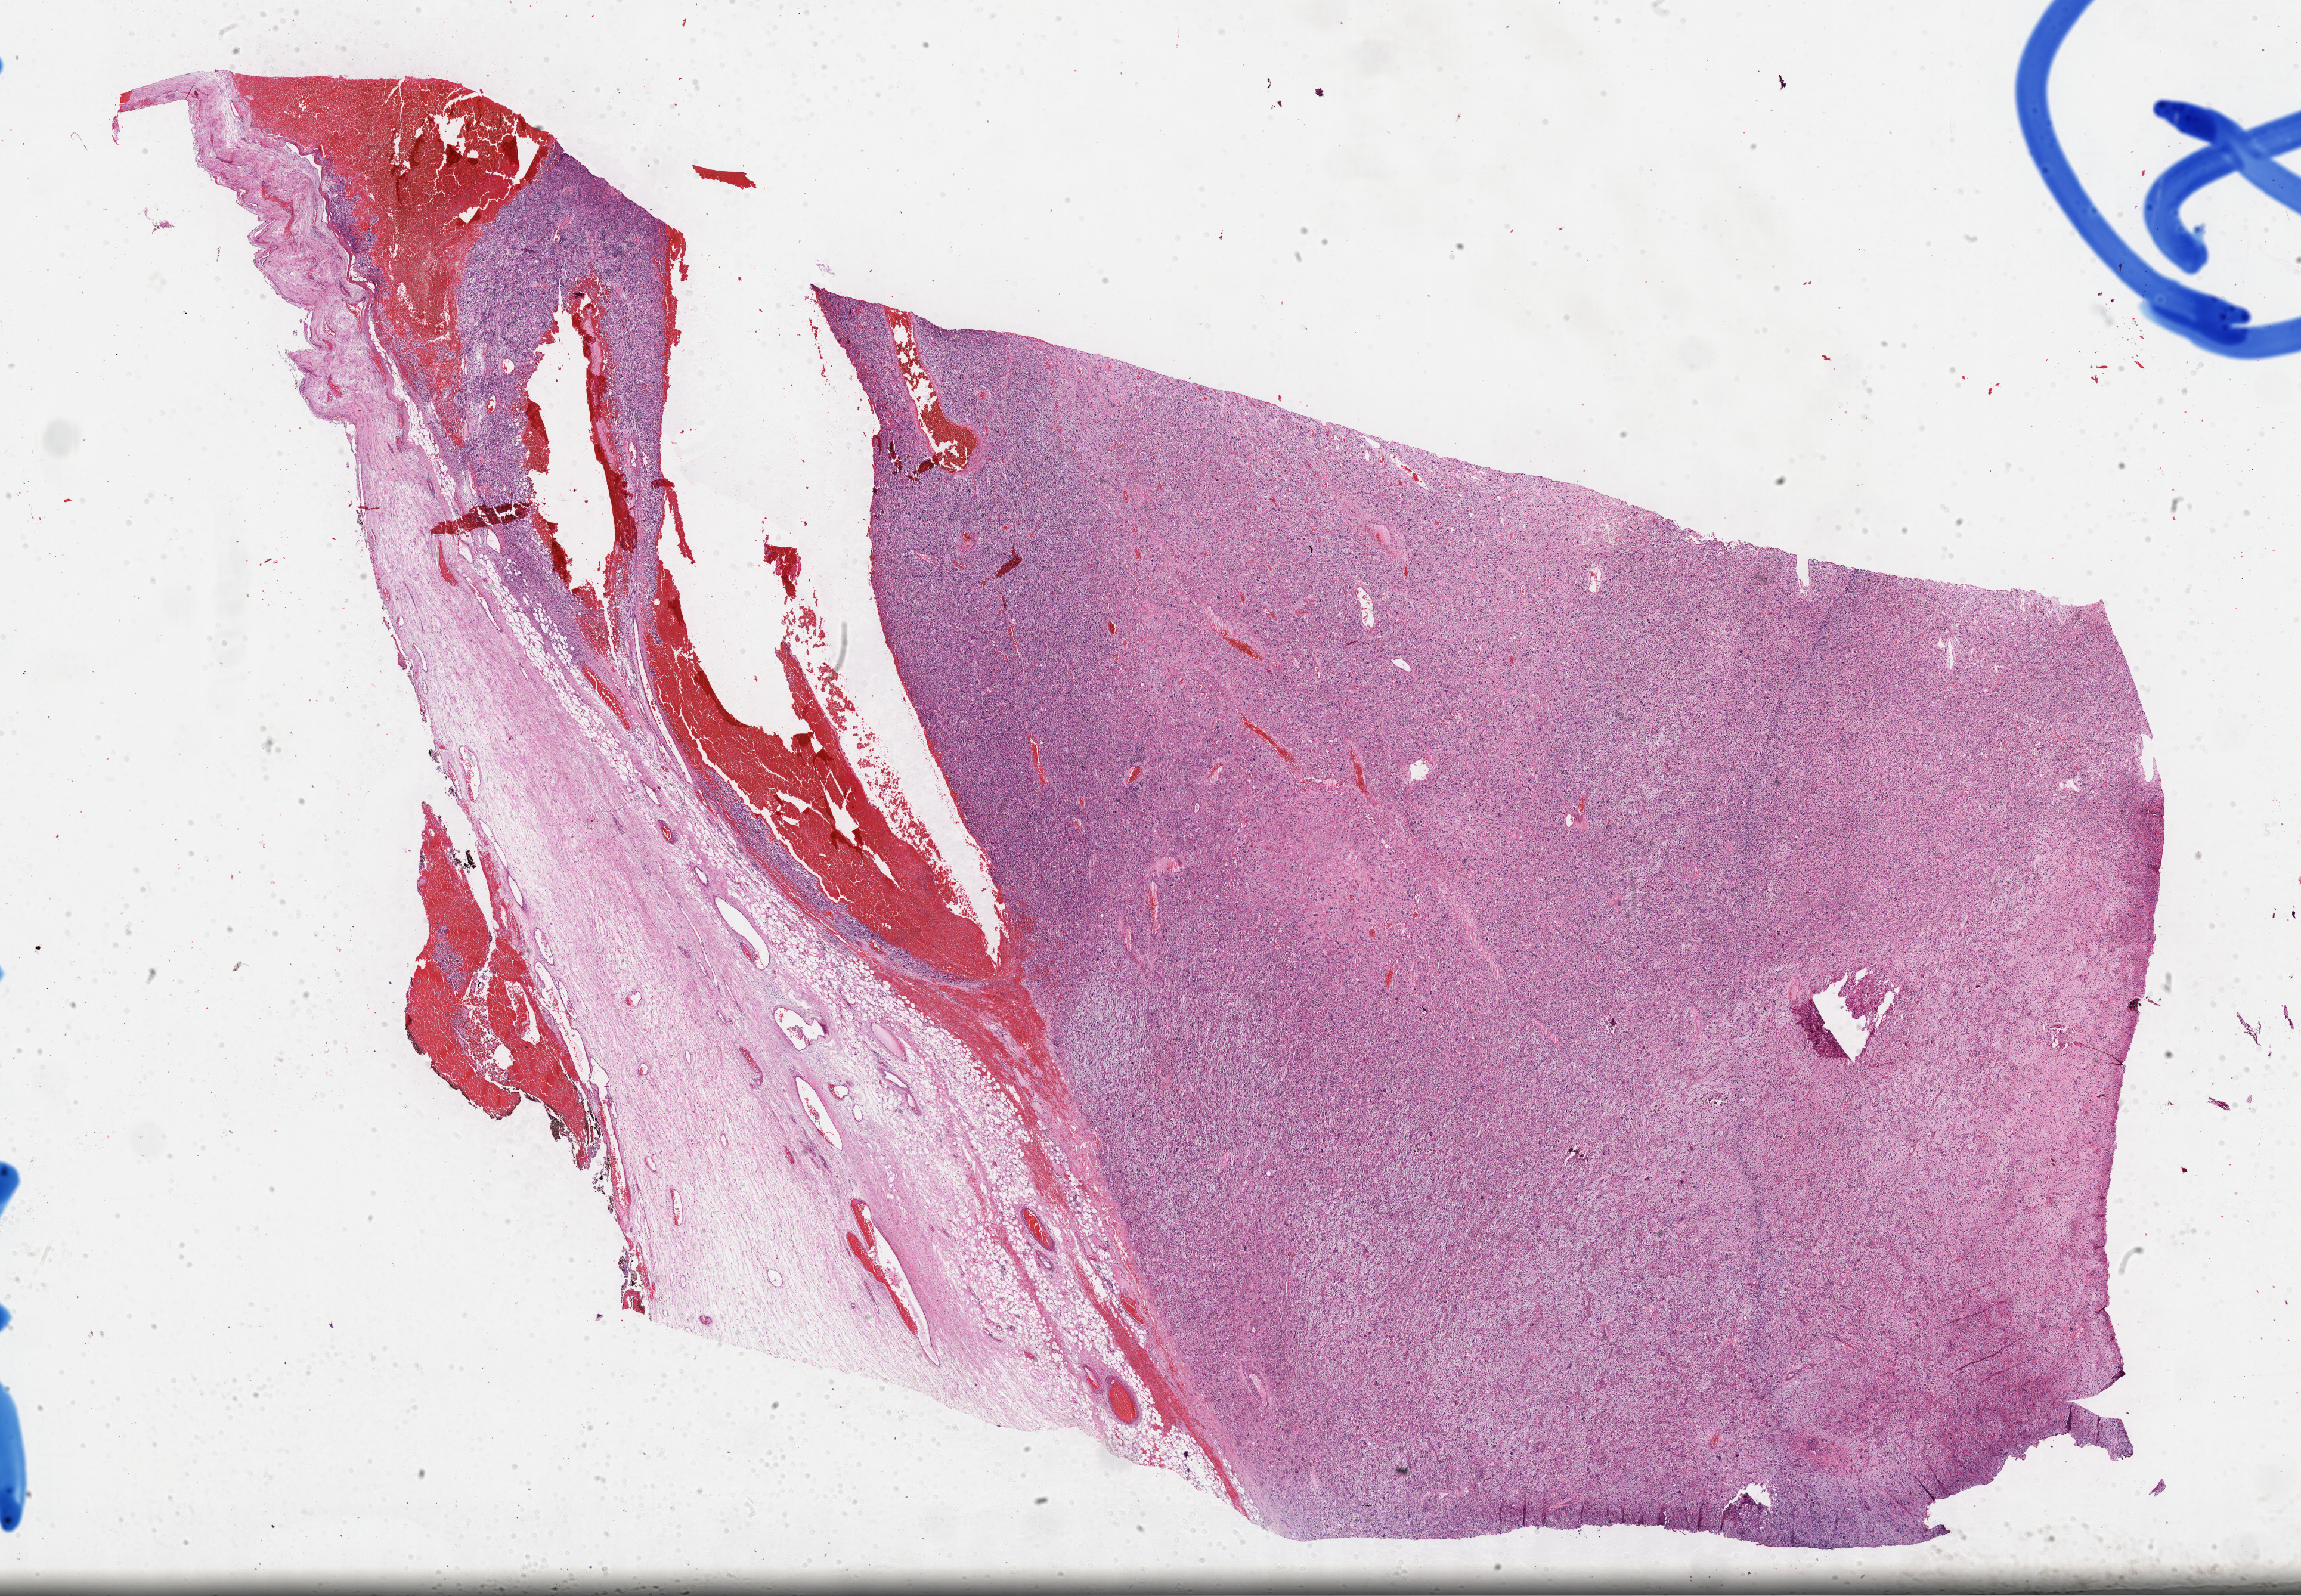
Whole-slide histology image, H&E — whole scanned area (about 31.2 x 21.6 mm, from a 40x scan) shown as a low-resolution overview; formalin-fixed paraffin-embedded (FFPE) diagnostic section; primary tumour sample from the adrenal cortex. Male, age 66 years at initial diagnosis.
* diagnosis: Adrenal cortical carcinoma (cortex of adrenal gland)
* lymph nodes positive (case pathology): 0 of 1 examined